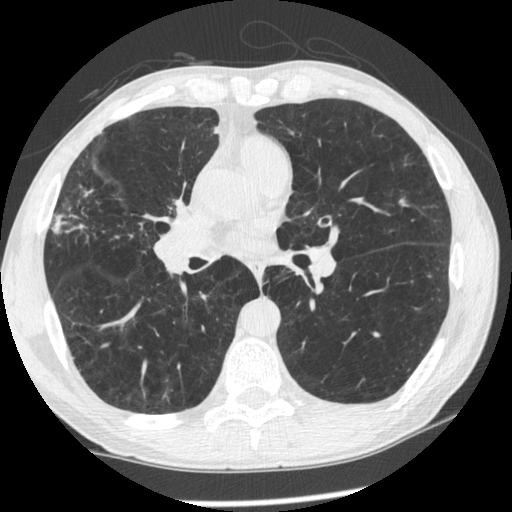
Low-dose screening chest CT, one axial slice; position 121 of 261 along the scan axis; reconstruction kernel STANDARD; 120 kVp; lung window (W 1500 / L -600 HU); 1.25 mm slice thickness; 512 × 512 image matrix, field of view 340 × 340 mm.
Annotated regions visible in this slice (outlined manually by an expert reader):
- lesion 1 (tumor, upper lobe of right lung): bounding box (x1, y1, x2, y2) in pixels: (174, 198, 186, 214)